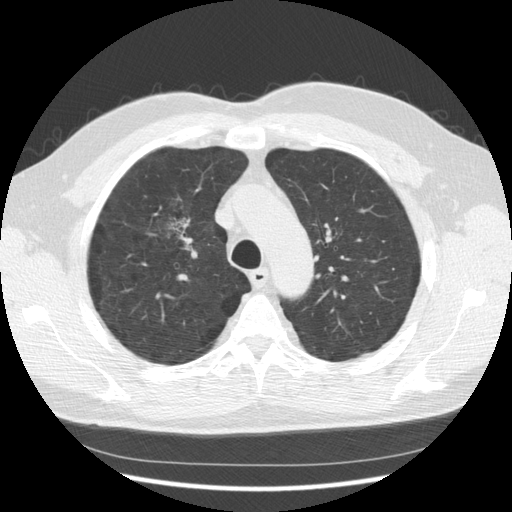
Low-dose screening chest CT, one axial slice. Reconstruction kernel STANDARD. Lung window (W 1500 / L -600 HU). 512 × 512 image matrix, field of view 369 × 369 mm.
Annotated regions visible in this slice (manually delineated by an expert):
- lesion 1 (tumor, upper lobe of right lung): bounding box (x1, y1, x2, y2) in pixels: (168, 218, 187, 241)